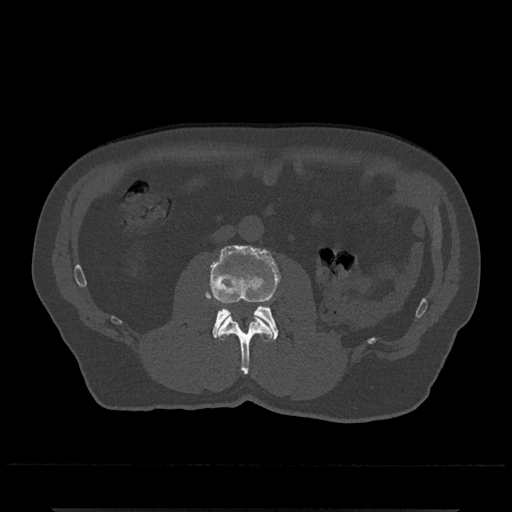
CT including the spine, one axial slice; slice 255 of 797 in the series (ordered by position); reconstruction kernel Br40s/3; 120 kVp; bone window (W 1800 / L 400 HU); 0.5 mm slice thickness; 512 × 512 image matrix. Patient: male, 67 years. Case-level facts recorded for this patient, not image findings: primary cancer: prostate.
Outlined on this slice (semi-automatic segmentation, software-assisted and operator-edited):
- L2 vertebra: bounding box [x1, y1, x2, y2] px = [217, 314, 273, 375]
- L3 vertebra: [206, 245, 280, 341]